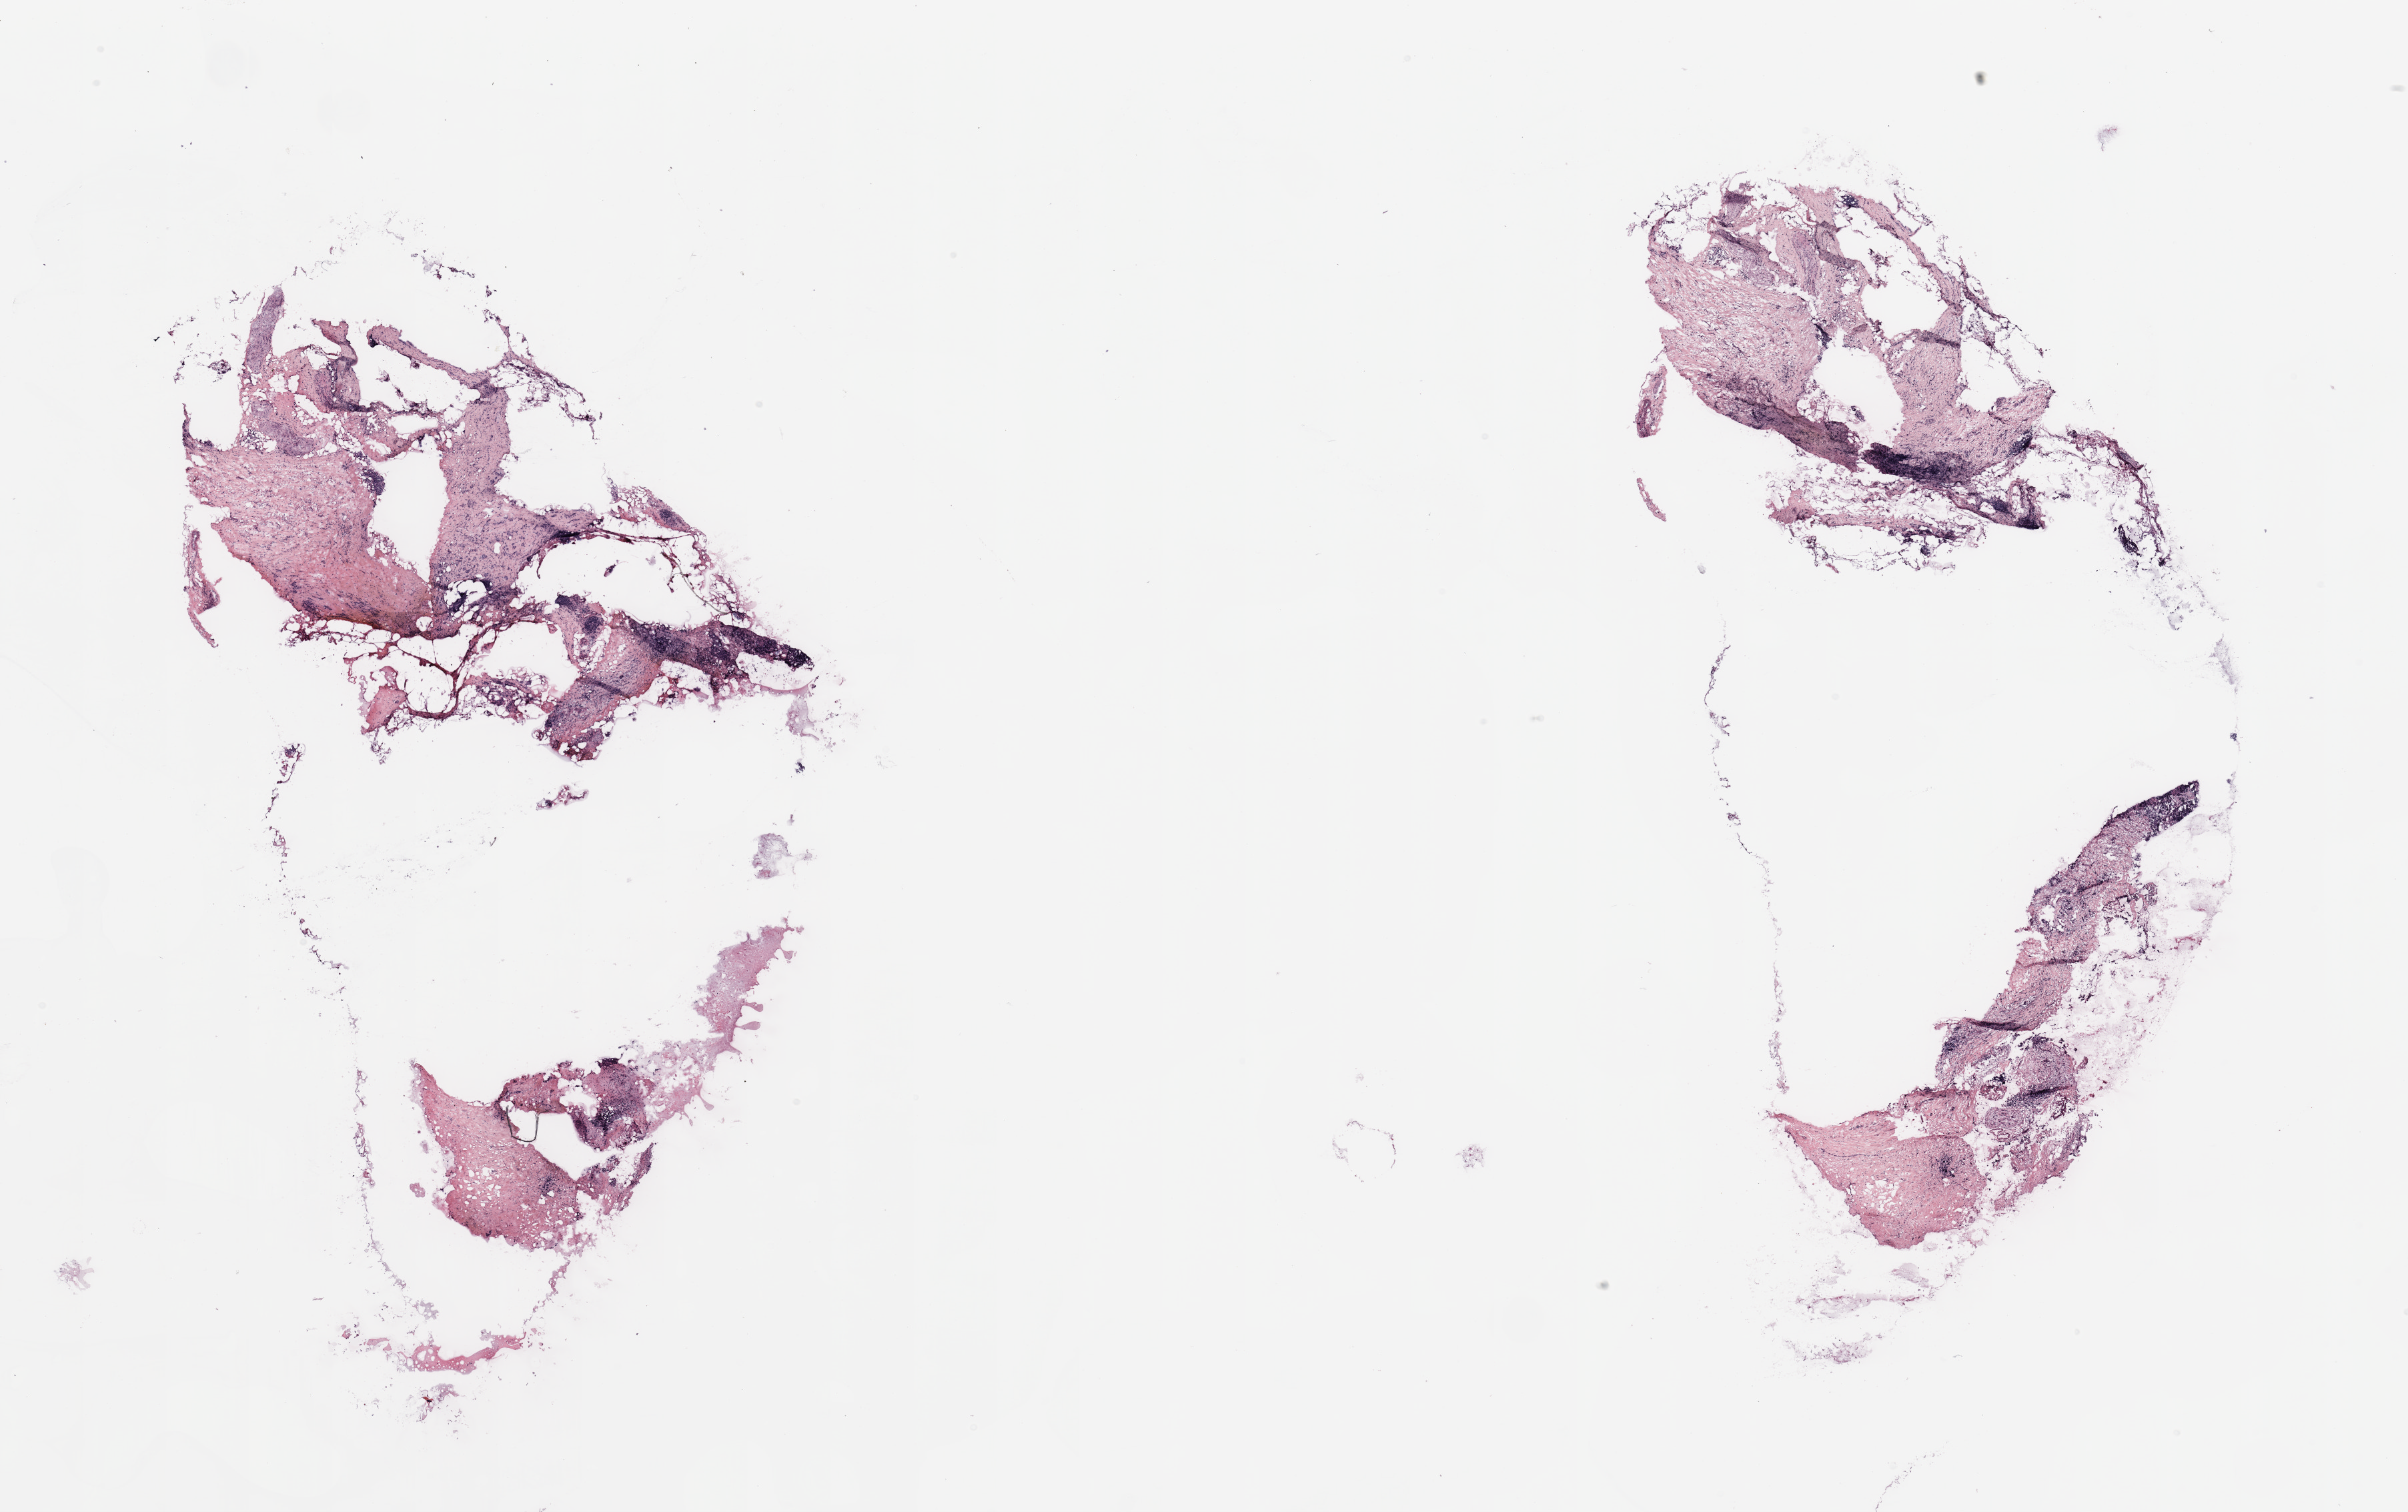
H&E whole-slide image — low-resolution overview of the scanned area, about 28.5 x 17.9 mm (from a 20x scan), breast, tissue type not recorded.
Patient diagnosis (cohort enrolment): breast cancer (breast).